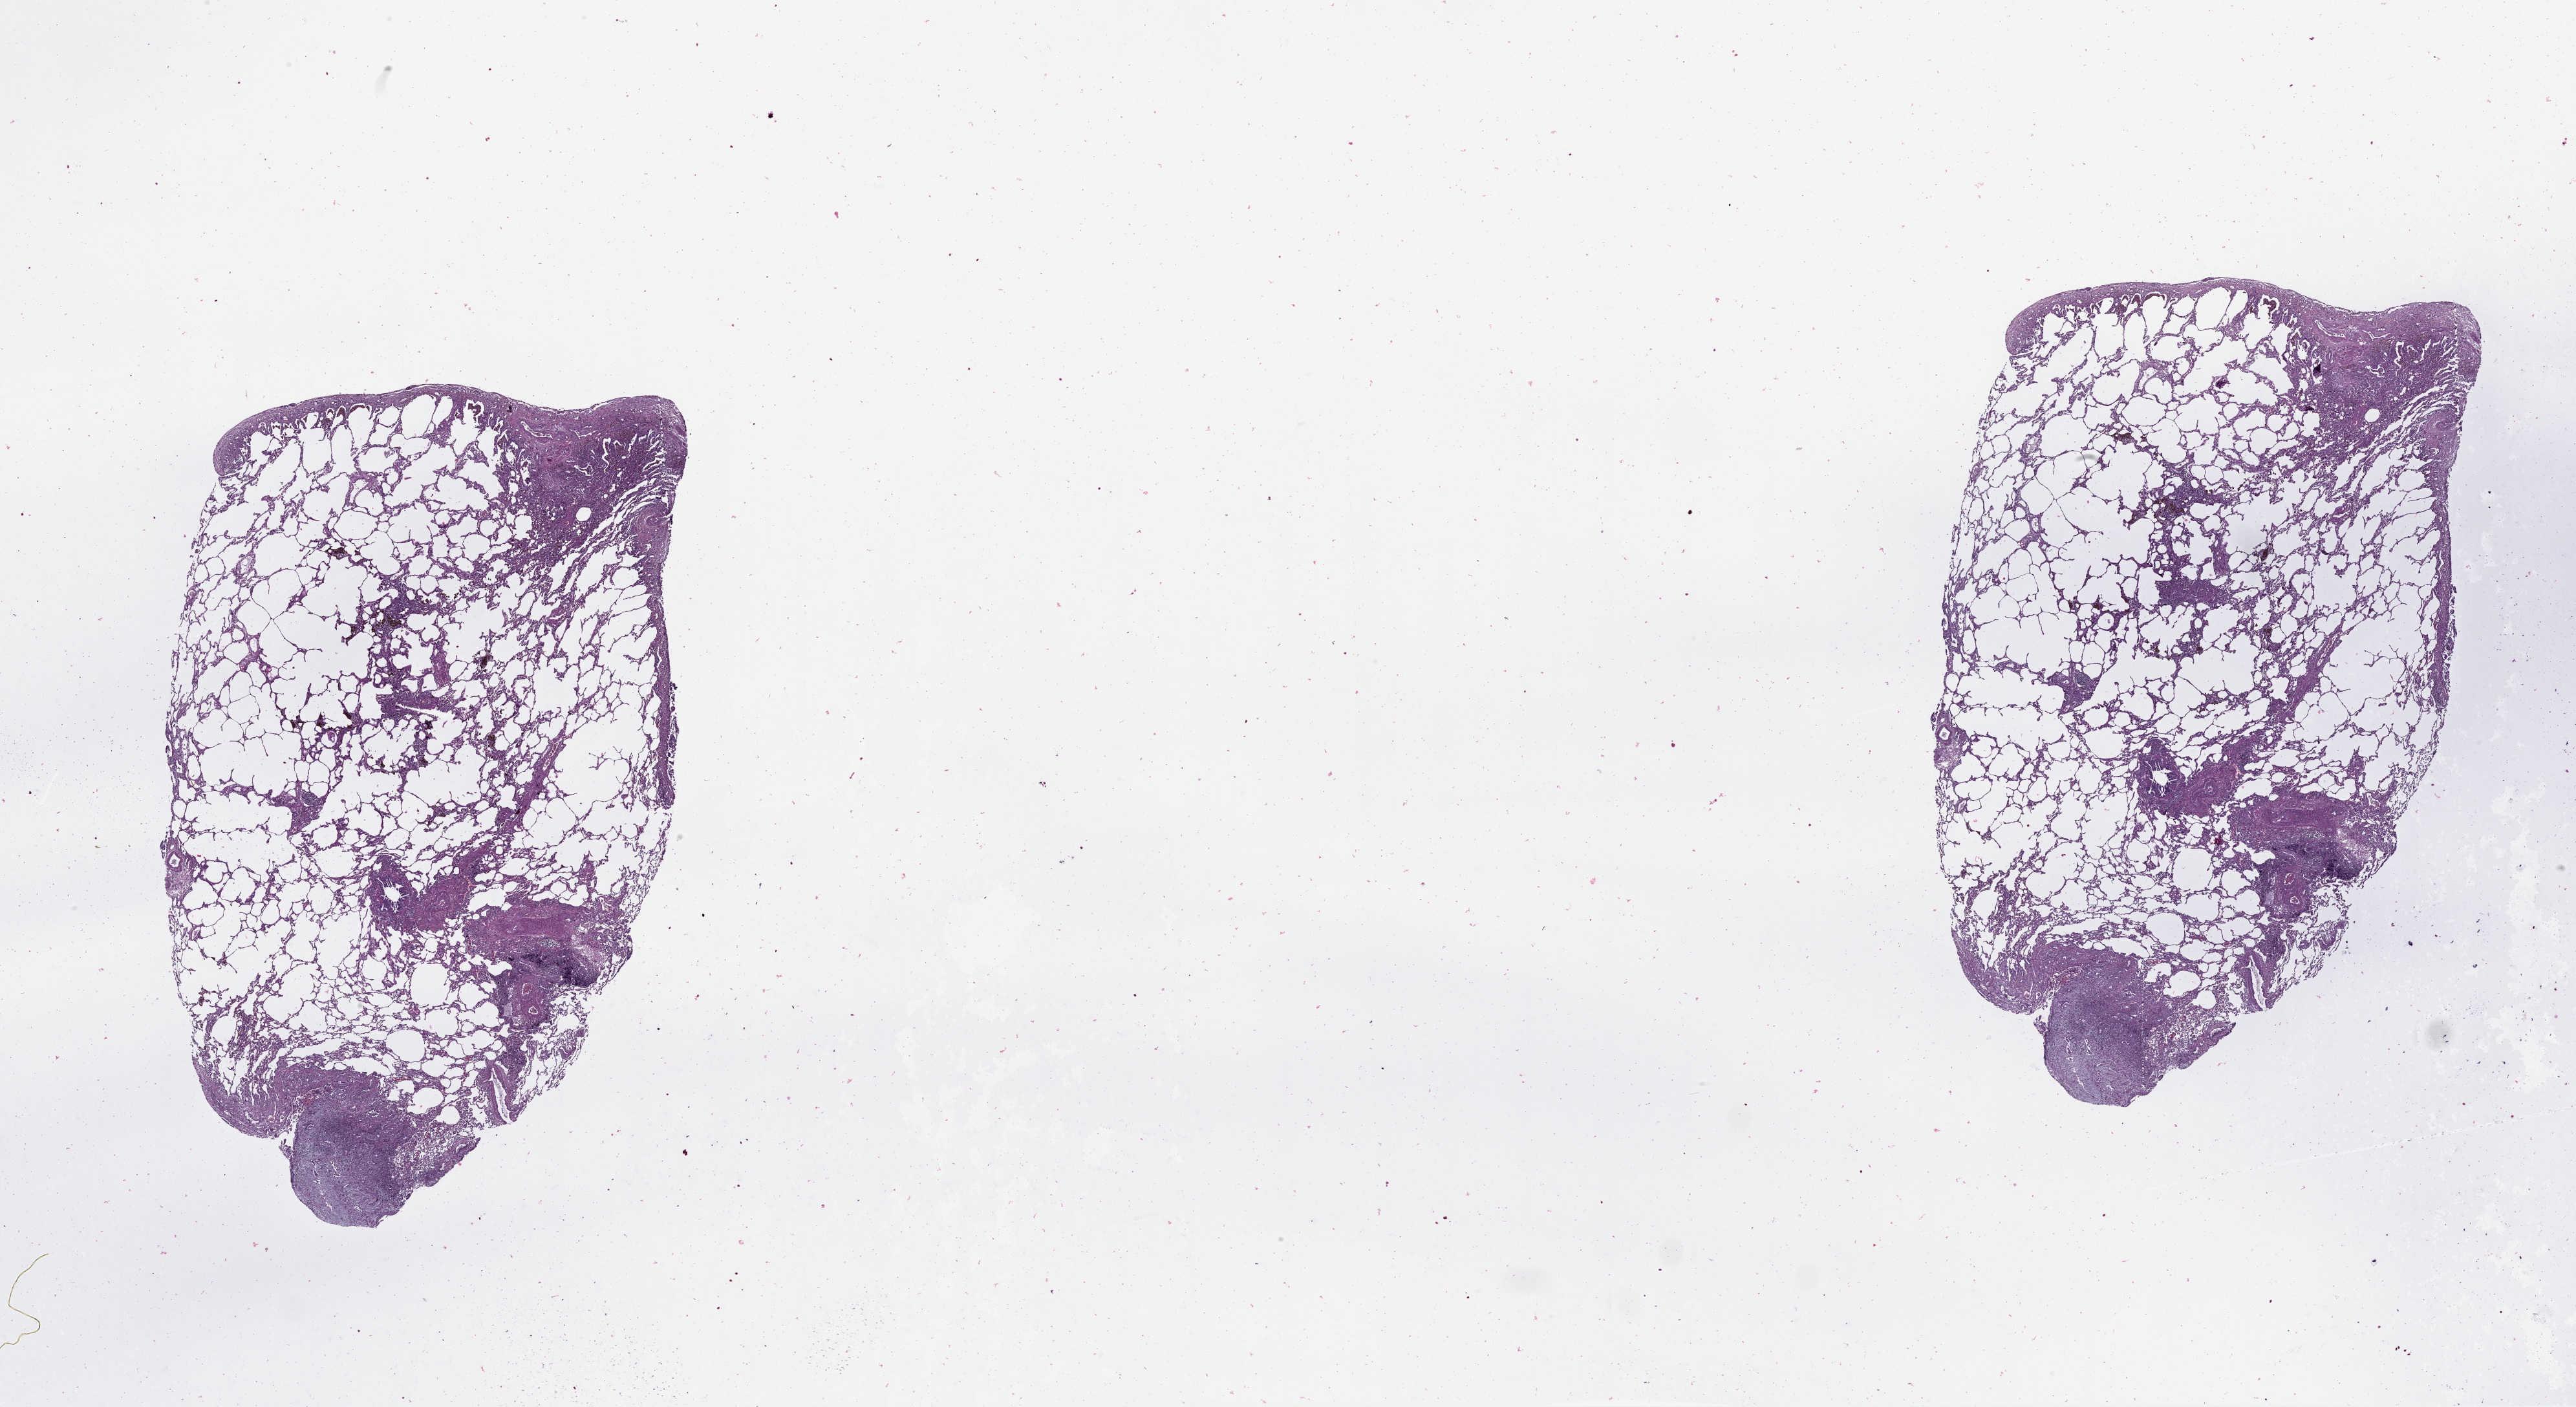
H&E whole-slide image — low-resolution overview of the scanned area, about 32.1 x 17.5 mm (acquisition: 20x scan); lung, tissue type not recorded.
Patient diagnosis (cohort enrolment): lung adenocarcinoma (lung).